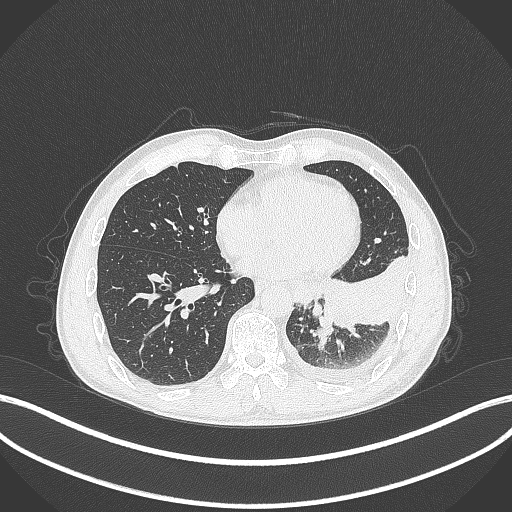
Chest CT, one axial slice; slice 105 of 295 in the series (ordered by position); reconstruction kernel B70f; 120 kVp; lung window (W 1500 / L -600 HU); 1 mm slice thickness; 512 × 512 image matrix, field of view 400 × 400 mm. Male patient, age 47 years. Case-level facts recorded for this patient, not image findings: clinical TNM (as recorded): T3 N1 M1c.
Annotated regions visible in this slice (bounding box drawn by a radiologist):
- lung tumour (recorded histology: small cell carcinoma): box from (x=310, y=311) to (x=335, y=327) px